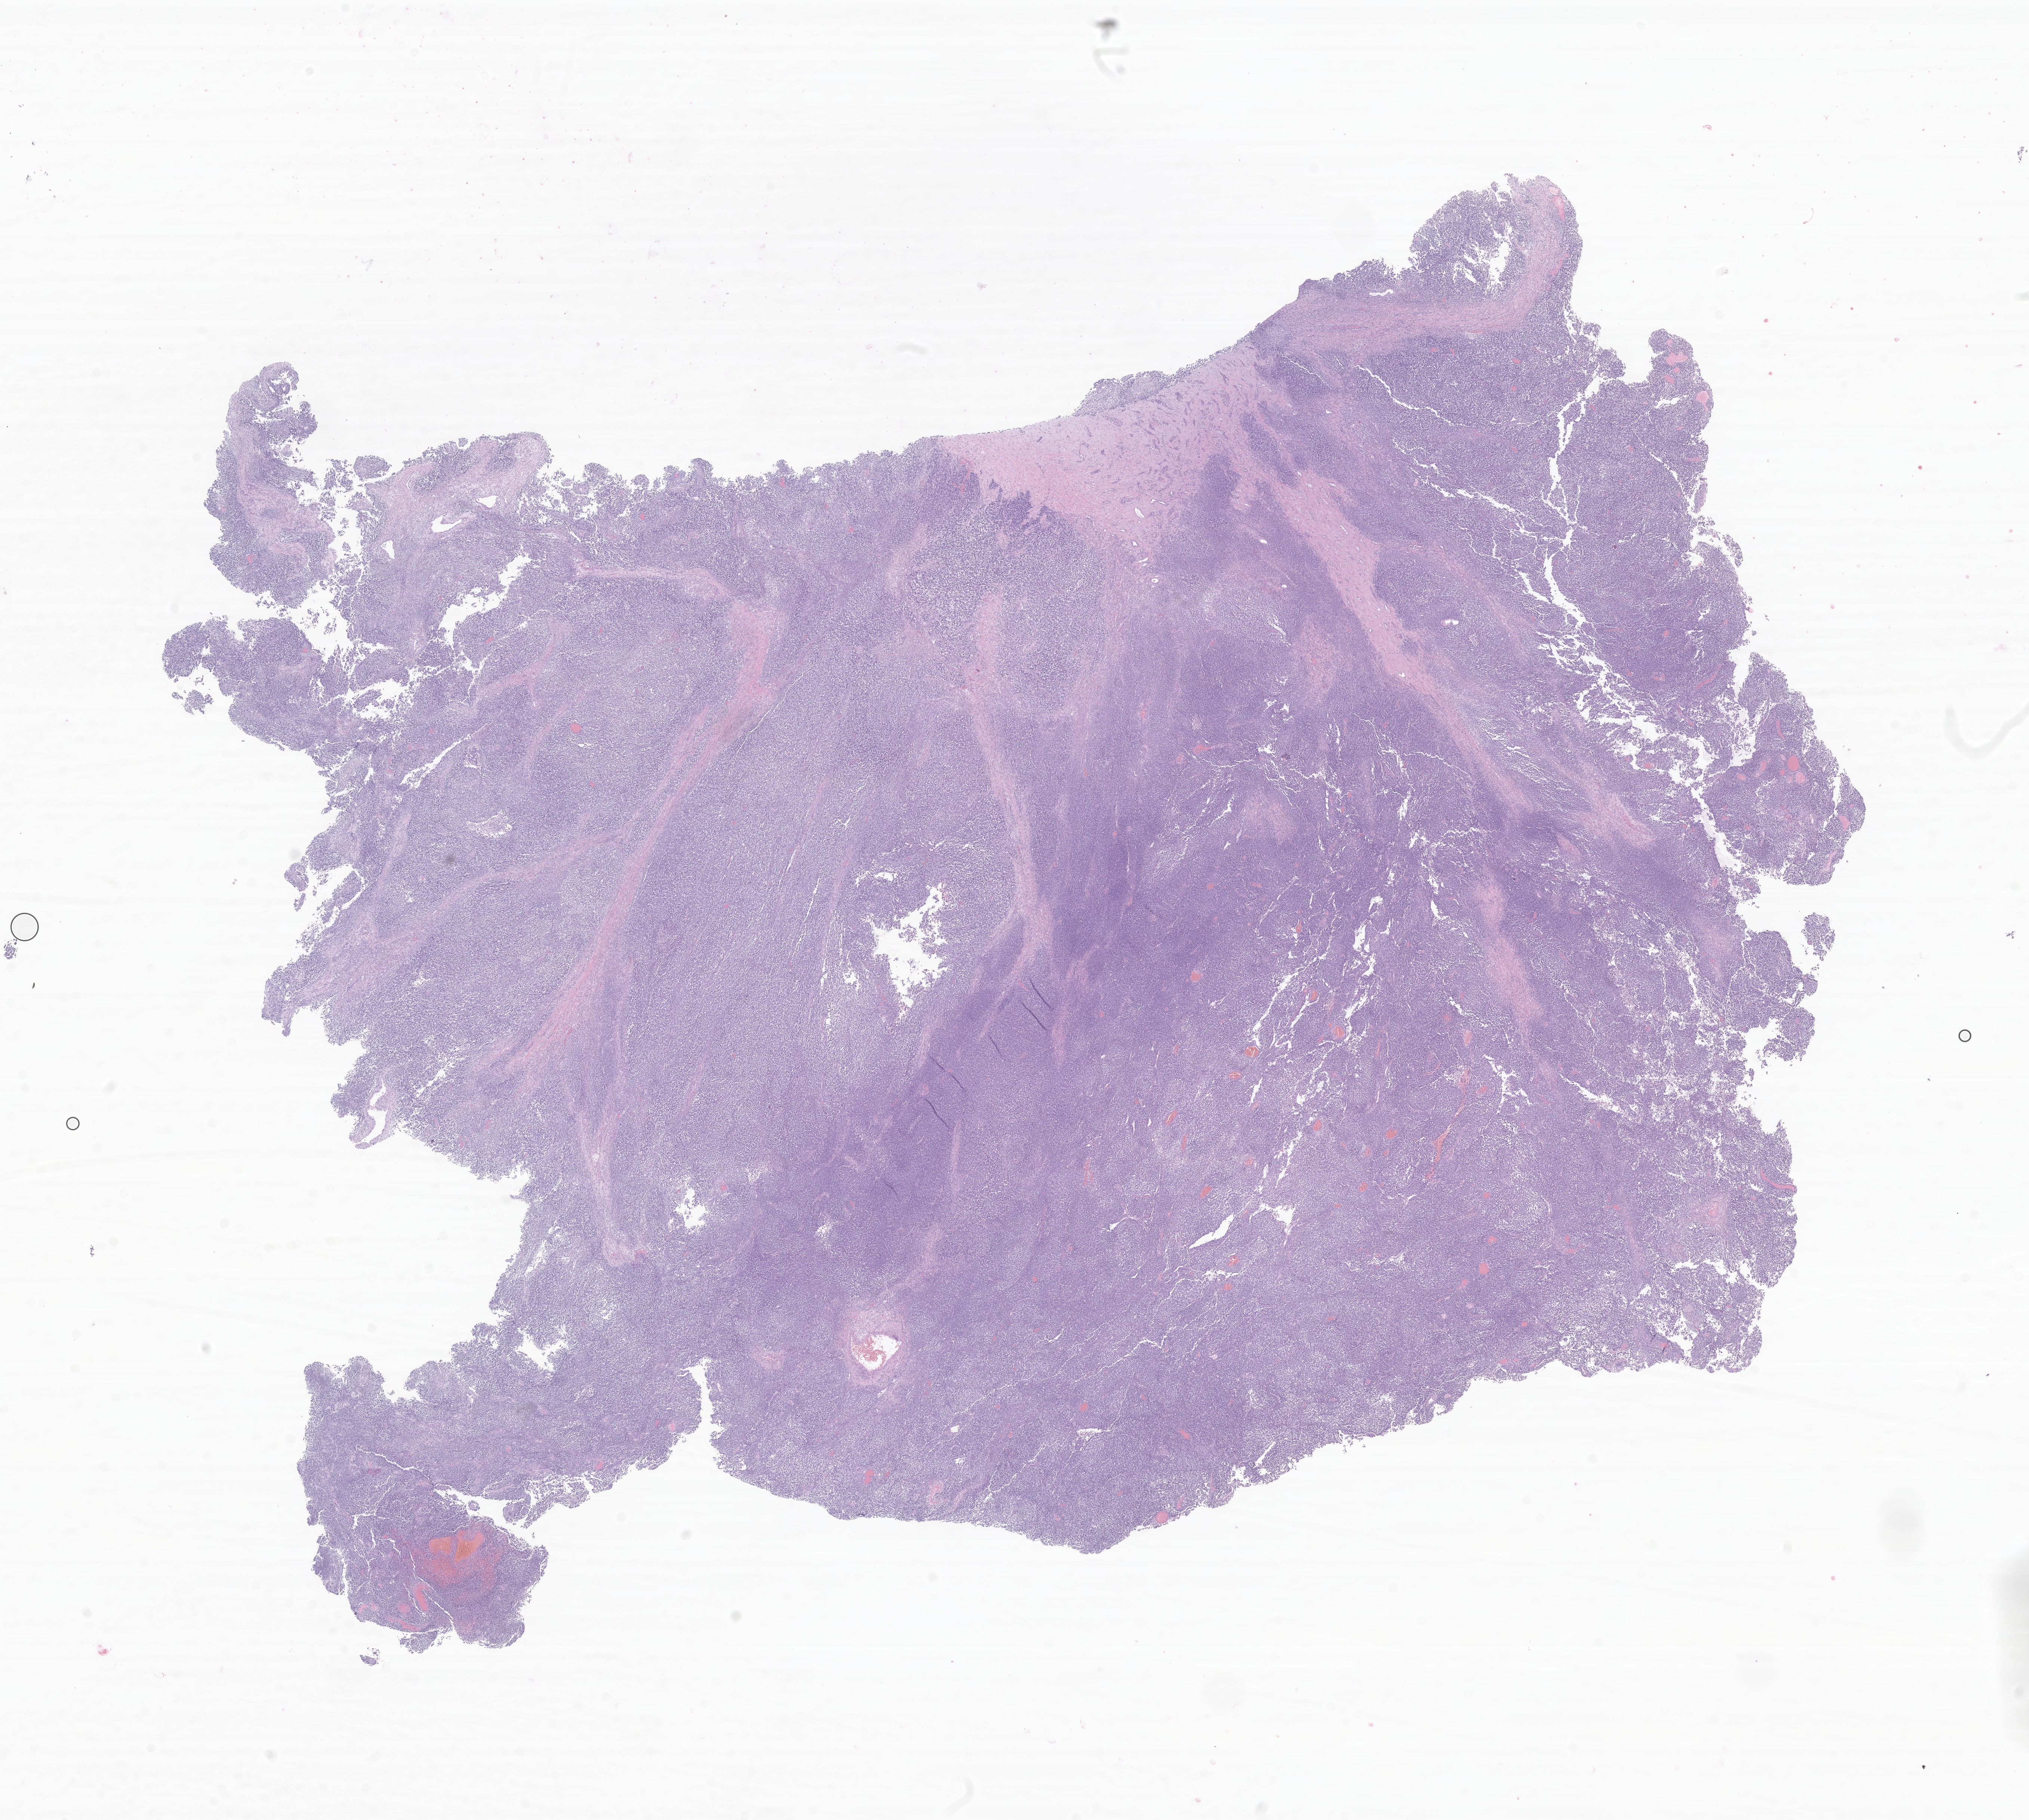
Whole-slide image, H&E stain of tumor tissue from the kidney, a low-resolution overview of the entire scanned area, about 22.9 x 20.5 mm. FFPE section. Female patient, age 167 months (13 years 11 months).
Diagnosis (ICD-O-3 morphology term): Small cell sarcoma.